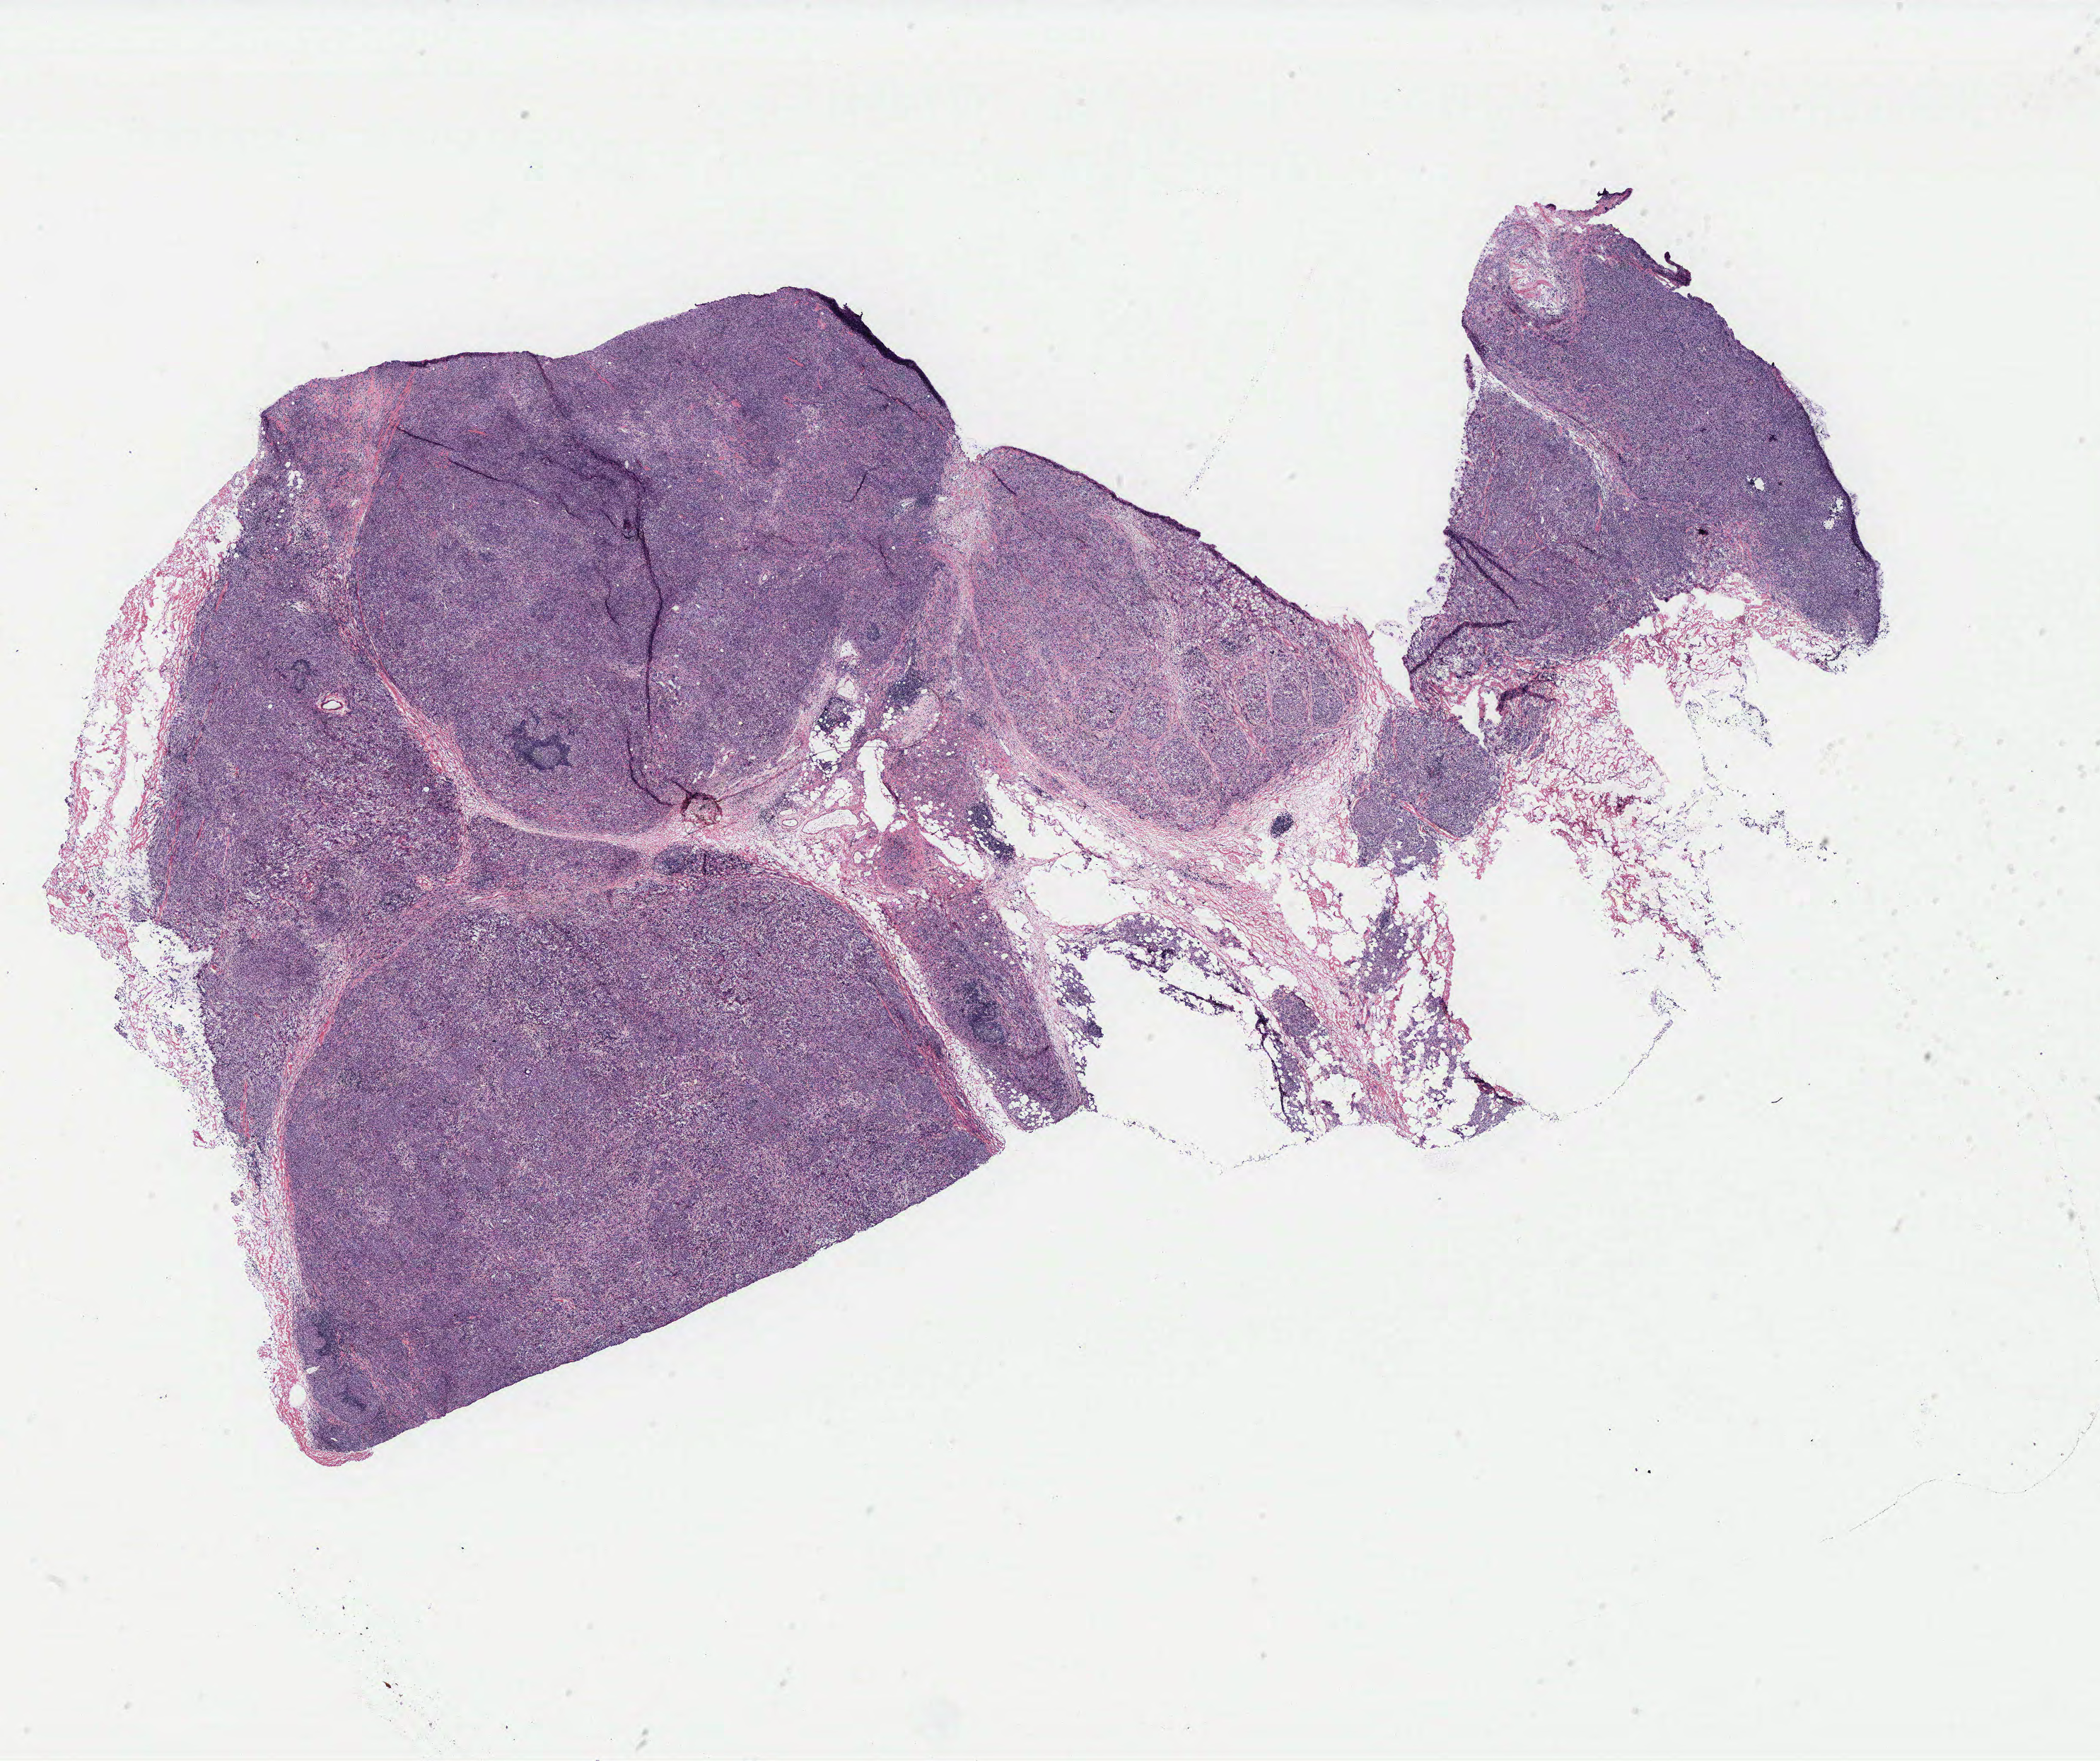
Whole-slide histology image, Hematoxylin and eosin (H&E) stained, whole scanned area (about 23.8 x 19.9 mm, slide scanned at 40x) shown as a low-resolution overview; breast, tissue type not recorded. 60-year-old female patient.
Patient diagnosis: Infiltrating duct and lobular carcinoma.